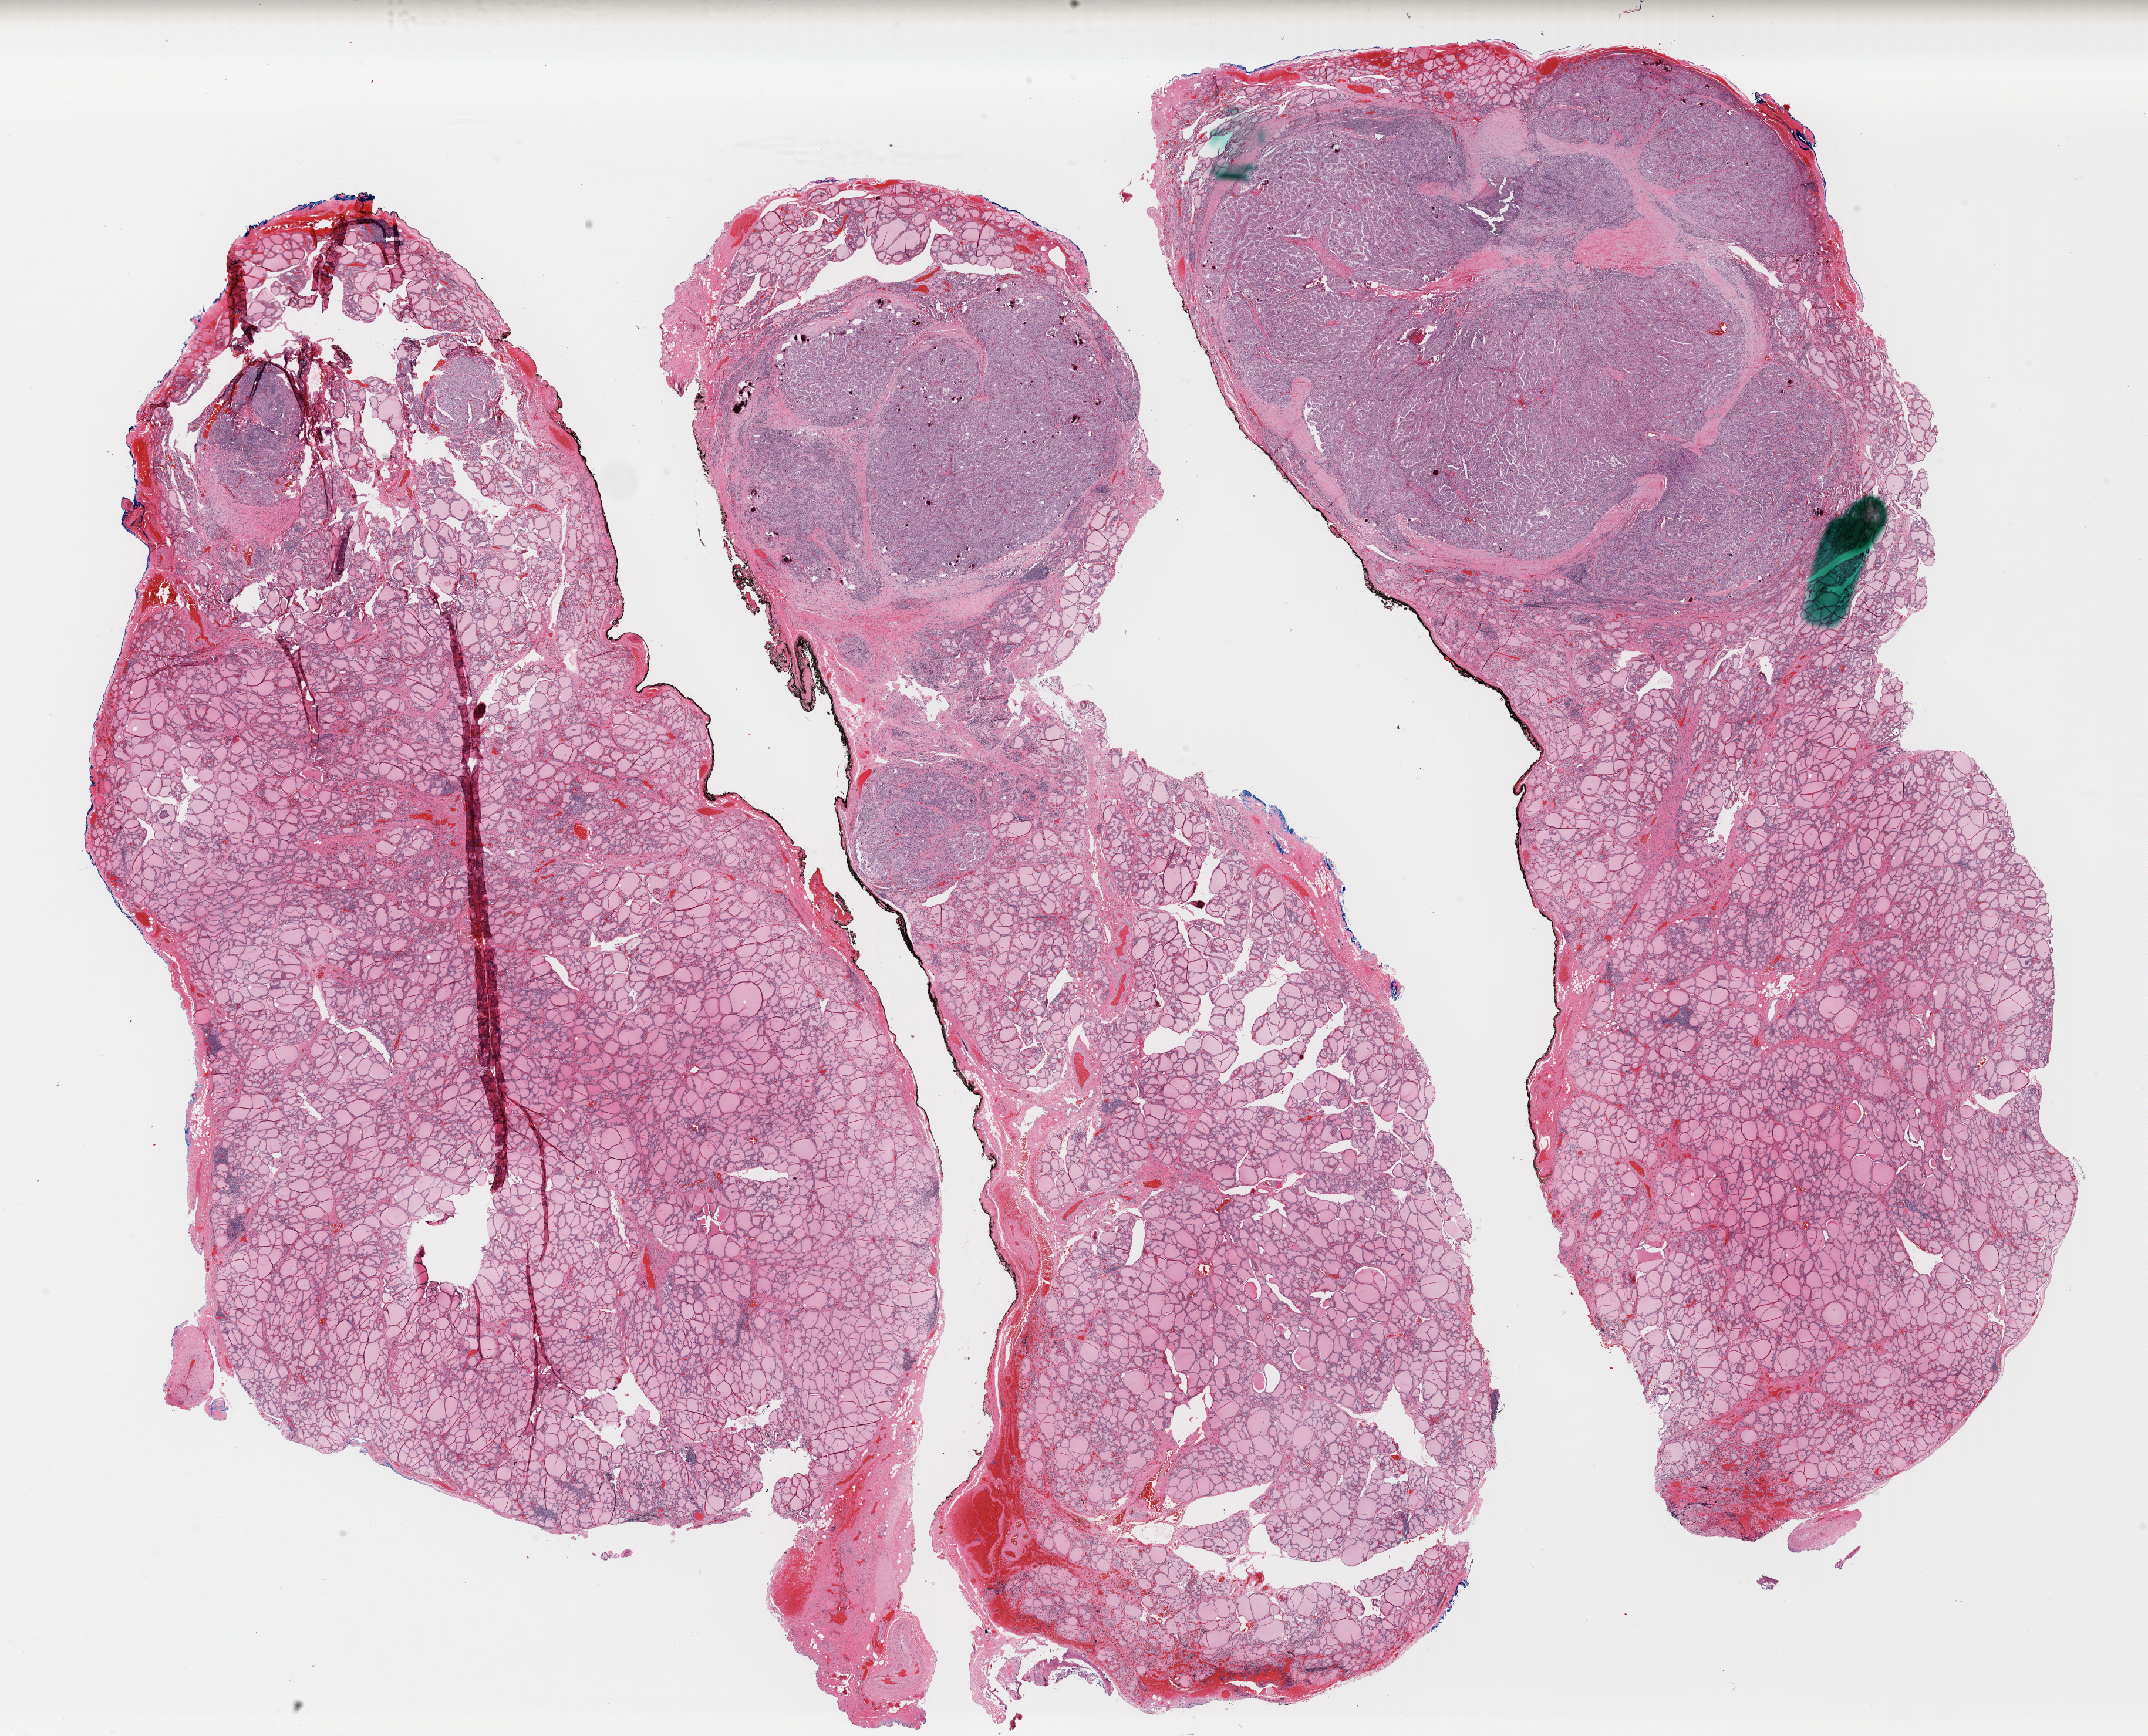
Digitized H&E-stained tissue section (whole slide), a low-resolution overview of the entire scanned area, about 28.8 x 23.2 mm (slide scanned at 40x); formalin-fixed paraffin-embedded (FFPE) diagnostic section; thyroid, primary tumour sample. Female patient; age at initial diagnosis 32 years.
Pathologic diagnosis: Papillary adenocarcinoma, NOS (thyroid gland).